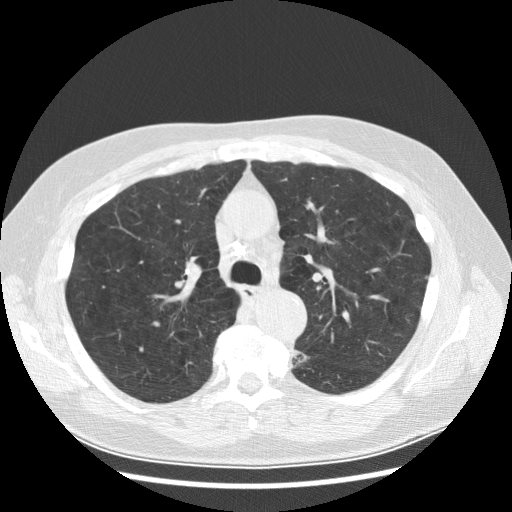
Low-dose screening chest CT, one axial slice; position 195 of 282 along the scan axis; reconstruction kernel STANDARD; 120 kVp; lung window (W 1500 / L -600 HU); 2.5 mm slice thickness; 512 × 512 image matrix, field of view 370 × 370 mm.
Structures marked on this image (expert manual segmentation):
- lesion 1 (tumor, lower lobe of left lung): bounding box (x1, y1, x2, y2) in pixels: (294, 350, 309, 365)